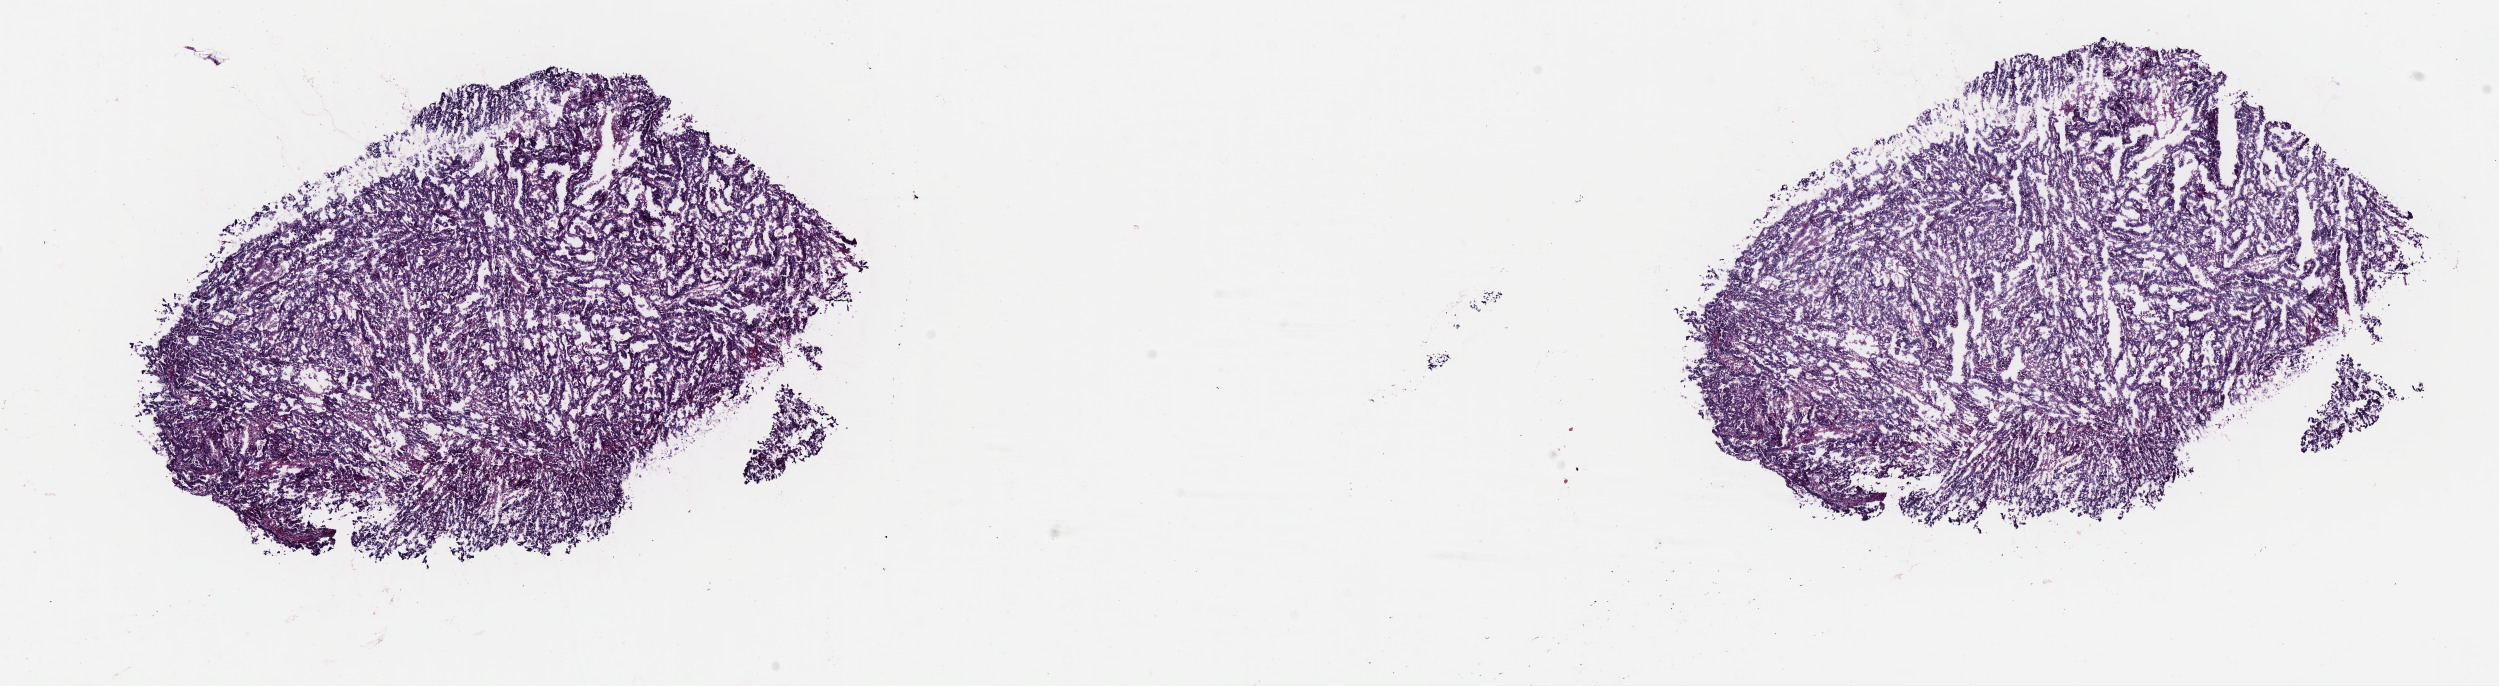
Whole-slide histology image, H&E-stained, a low-resolution overview of the entire scanned area, about 19.7 x 5.4 mm. Frozen section. Sample: primary tumour, uterus. Patient: female, age at initial diagnosis 67 years. Histologic grade: G2 (moderately differentiated). Pathologist review of this section (percent, as recorded): tumour cells 90%, tumour nuclei 94%, normal cells 0%, stromal cells 2%, necrosis 8%. Infiltration values recorded for this section: lymphocyte infiltration 1%, monocyte infiltration 0%, neutrophil infiltration 1%.
- FIGO stage: IA
- histologic diagnosis: Serous cystadenocarcinoma, NOS (endometrium)